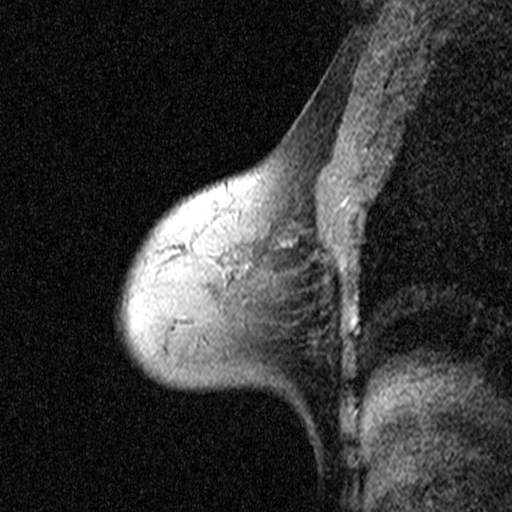
Breast MRI (dynamic contrast-enhanced), one sagittal slice. Position 29 of 44 along the scan axis. Dynamic contrast-enhanced study with each time point stored as its own series, time point 2 of 3 at this slice position (early post-contrast, ordered by acquisition time). 1.5 T. TE 4.5 ms, TR 11 ms. 512 × 512 image matrix. Patient: female, 53 years. From the clinical record (not read from this slice): setting: breast cancer imaged before/during neoadjuvant chemotherapy; receptor status: HR-positive, HER2-negative.
Annotated regions visible in this slice (semi-automatically segmented with operator editing):
- analysis volume of interest (the breast-tissue region the enhancement analysis was run in; not a lesion): box from (x=186, y=216) to (x=307, y=311) px
- tumour enhancement mask (voxels above the 90 % enhancement threshold inside the analysis volume of interest): (x=228, y=243)–(x=292, y=268)